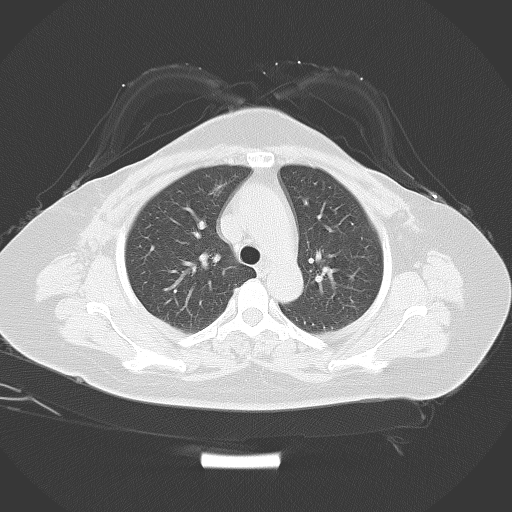
Chest CT, one axial slice; reconstruction kernel B70f; 120 kVp; lung window (W 1500 / L -600 HU); 5 mm slice thickness; 512 × 512 image matrix, field of view 410 × 410 mm. Patient: female, 55 years. Case-level facts recorded for this patient, not image findings: clinical TNM (as recorded): T2 N0 M0.
Outlined on this slice (rectangle marked by the reading radiologist):
- lung tumour (recorded histology: adenocarcinoma): bounding box (x1, y1, x2, y2) in pixels: (209, 174, 228, 200)